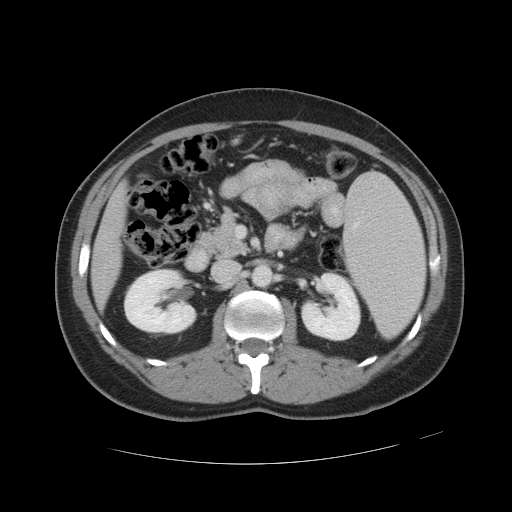
Contrast-enhanced abdominal CT, one axial slice; position 22 of 49 along the scan axis; reconstruction kernel STANDARD; intravenous contrast given; soft-tissue window (W 400 / L 40 HU); 5 mm slice thickness; 512 × 512 image matrix, field of view 422 × 422 mm. Male patient, age 42 years. Case-level facts recorded for this patient, not image findings: diagnosis: colorectal cancer liver metastases, imaged before liver resection.
Outlined on this slice (outlined manually by an expert reader):
- liver: bounding box [x1, y1, x2, y2] px = [93, 189, 125, 304]
- planned liver remnant (the part of the liver to remain after resection): [93, 236, 120, 305]